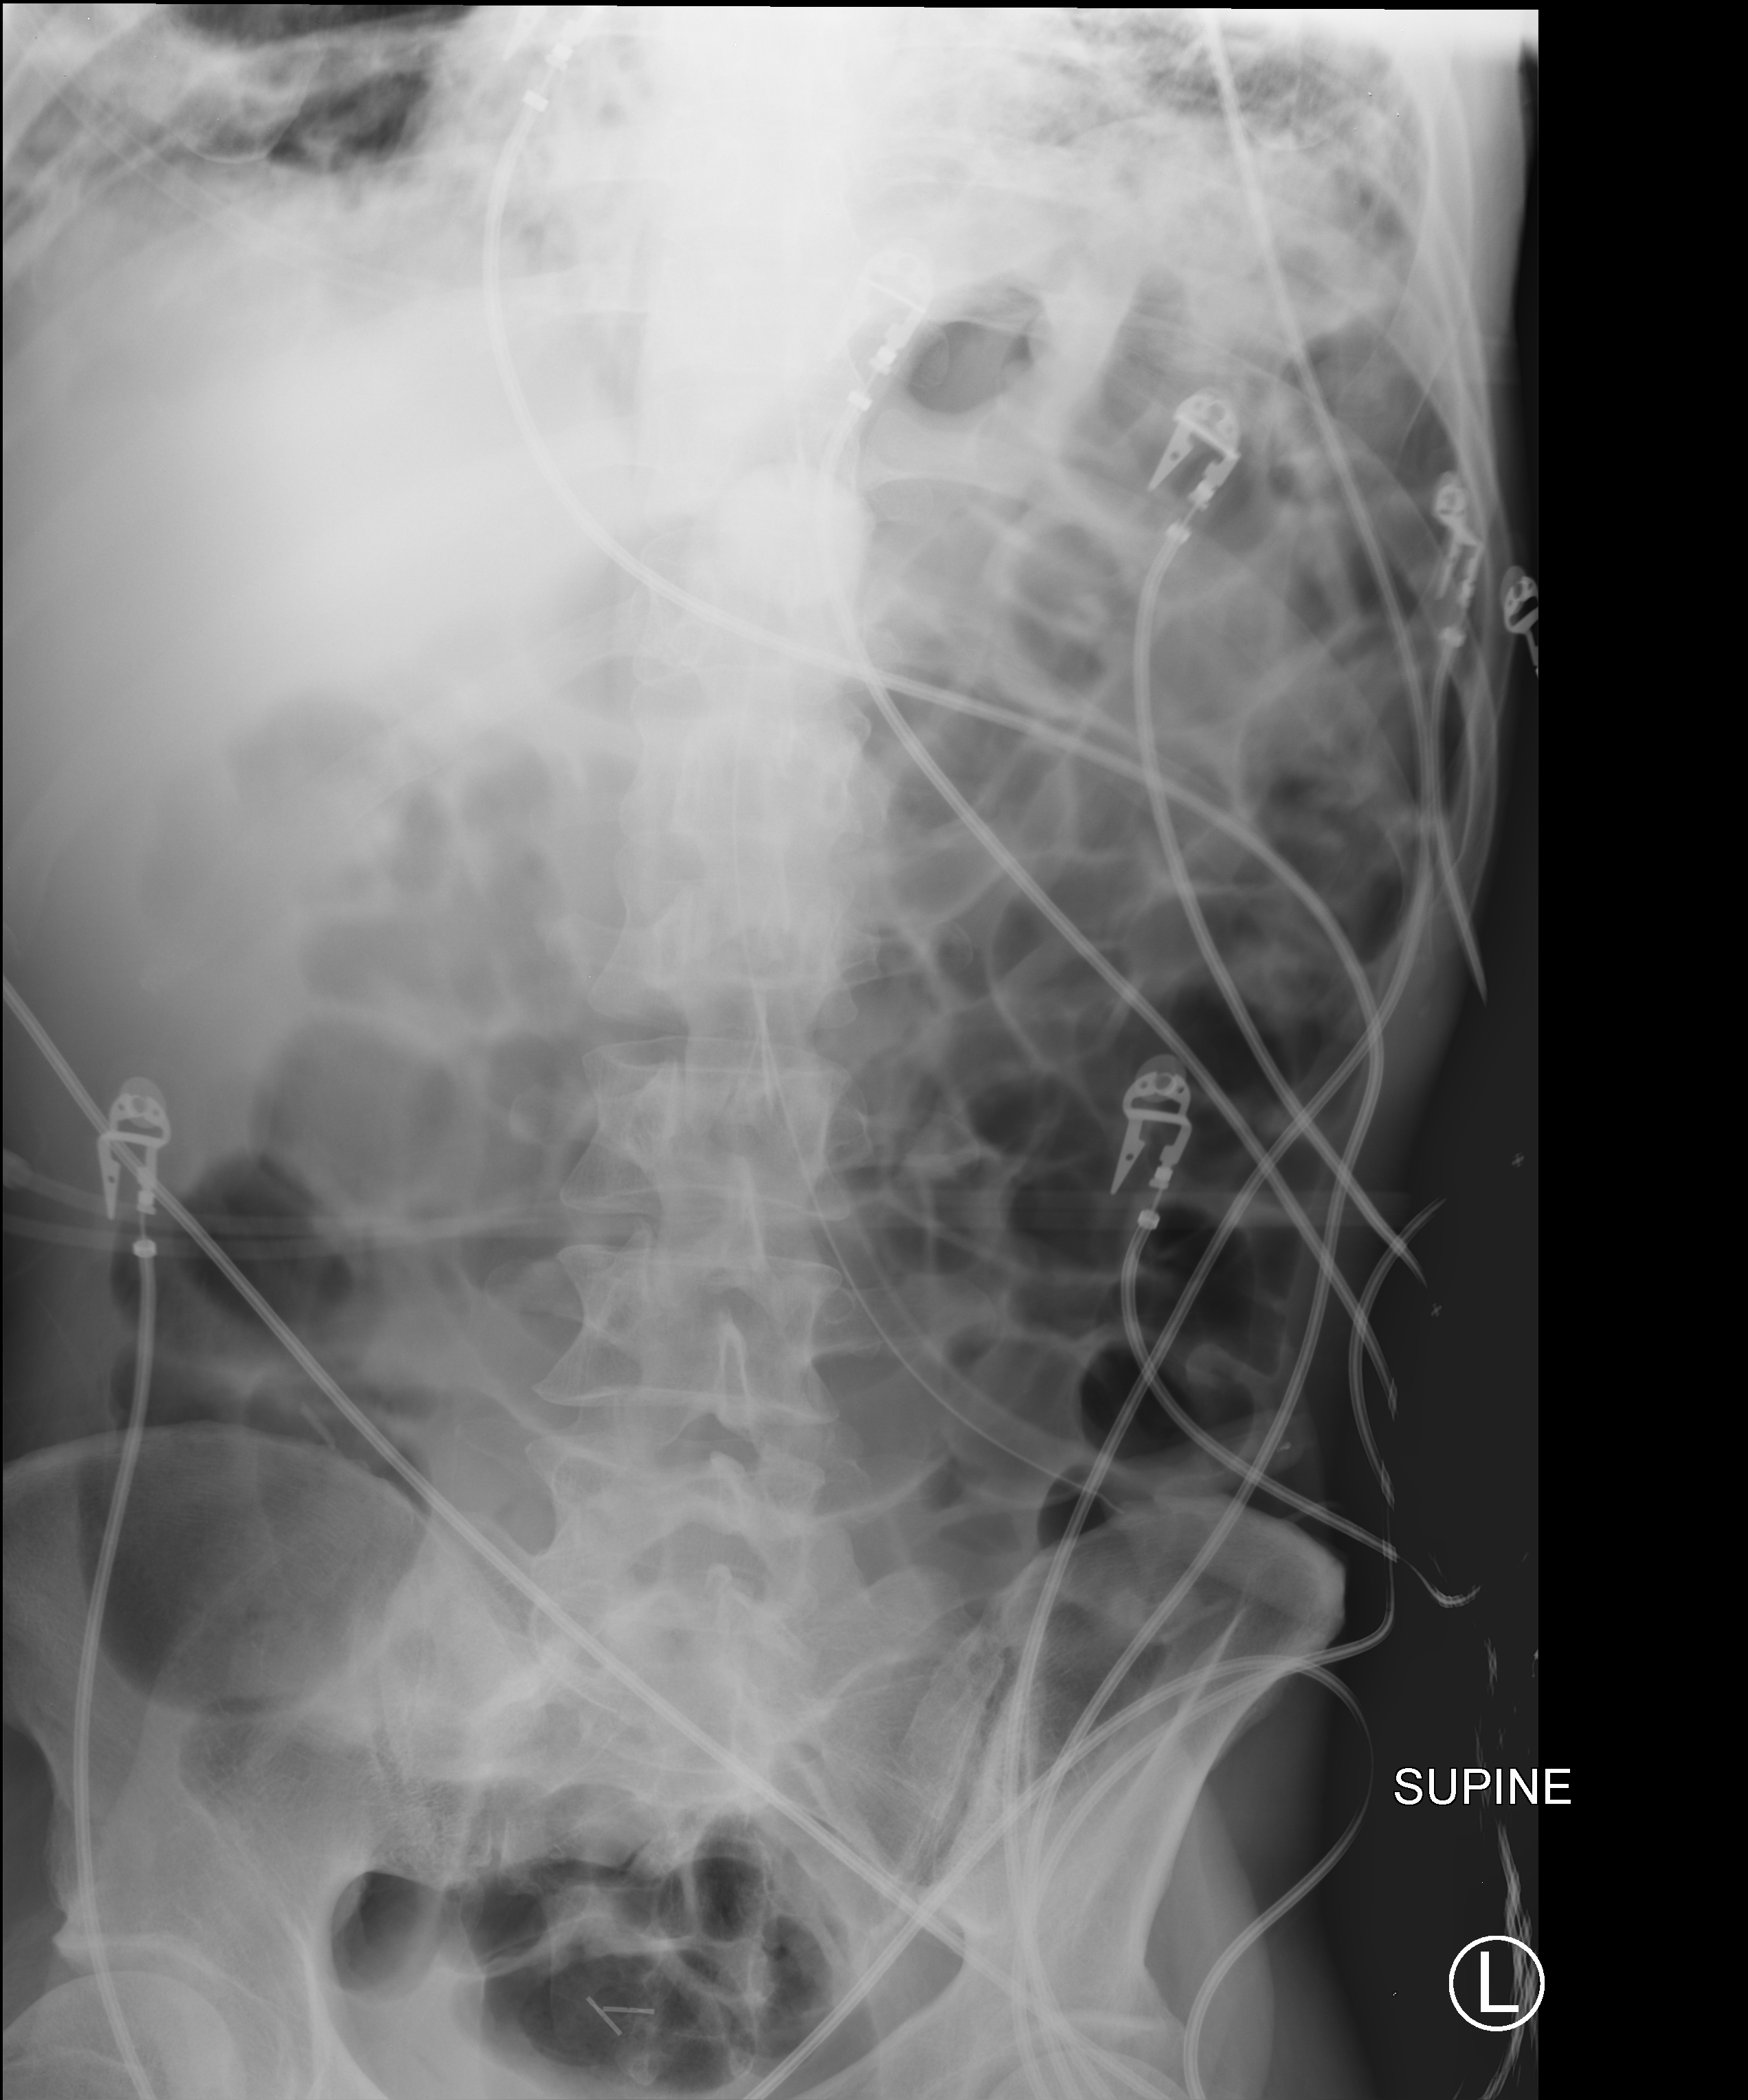
Abdomen X-ray (portable); anteroposterior (AP) projection. Patient hospitalised with COVID-19; male, aged 18–59 years.
From the hospital-stay record, not from the radiograph (when in the stay this image was taken is not recorded):
- admitted to intensive care during this hospital stay: yes